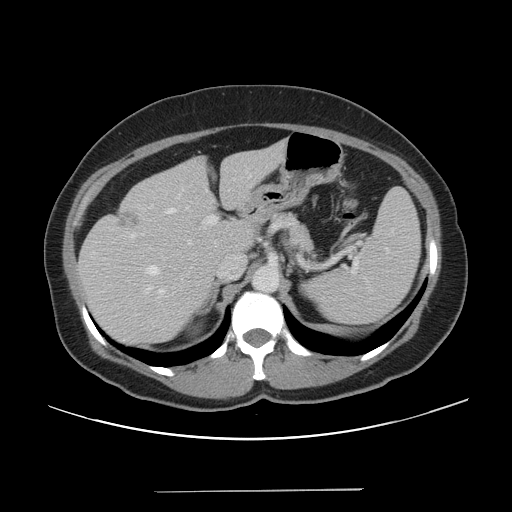
Contrast-enhanced abdominal CT, one axial slice. Slice 29 of 56 in the series (ordered by position). Soft-tissue window (W 400 / L 40 HU). 5 mm slice thickness. 512 × 512 image matrix, field of view 419 × 419 mm. Female patient, age 54 years. Case-level facts recorded for this patient, not image findings: diagnosis: colorectal cancer liver metastases, imaged before liver resection; multiple liver metastases: yes; largest metastasis: 3.2 cm; disease in both lobes: yes.
Outlined on this slice (manually delineated by an expert):
- hepatic veins: box from (x=148, y=192) to (x=189, y=274) px
- liver: (x=79, y=139)–(x=289, y=346)
- planned liver remnant (the part of the liver to remain after resection): (x=178, y=140)–(x=289, y=254)
- portal vein (with intrahepatic branches): (x=159, y=178)–(x=241, y=294)
- liver metastasis: (x=118, y=211)–(x=138, y=228)